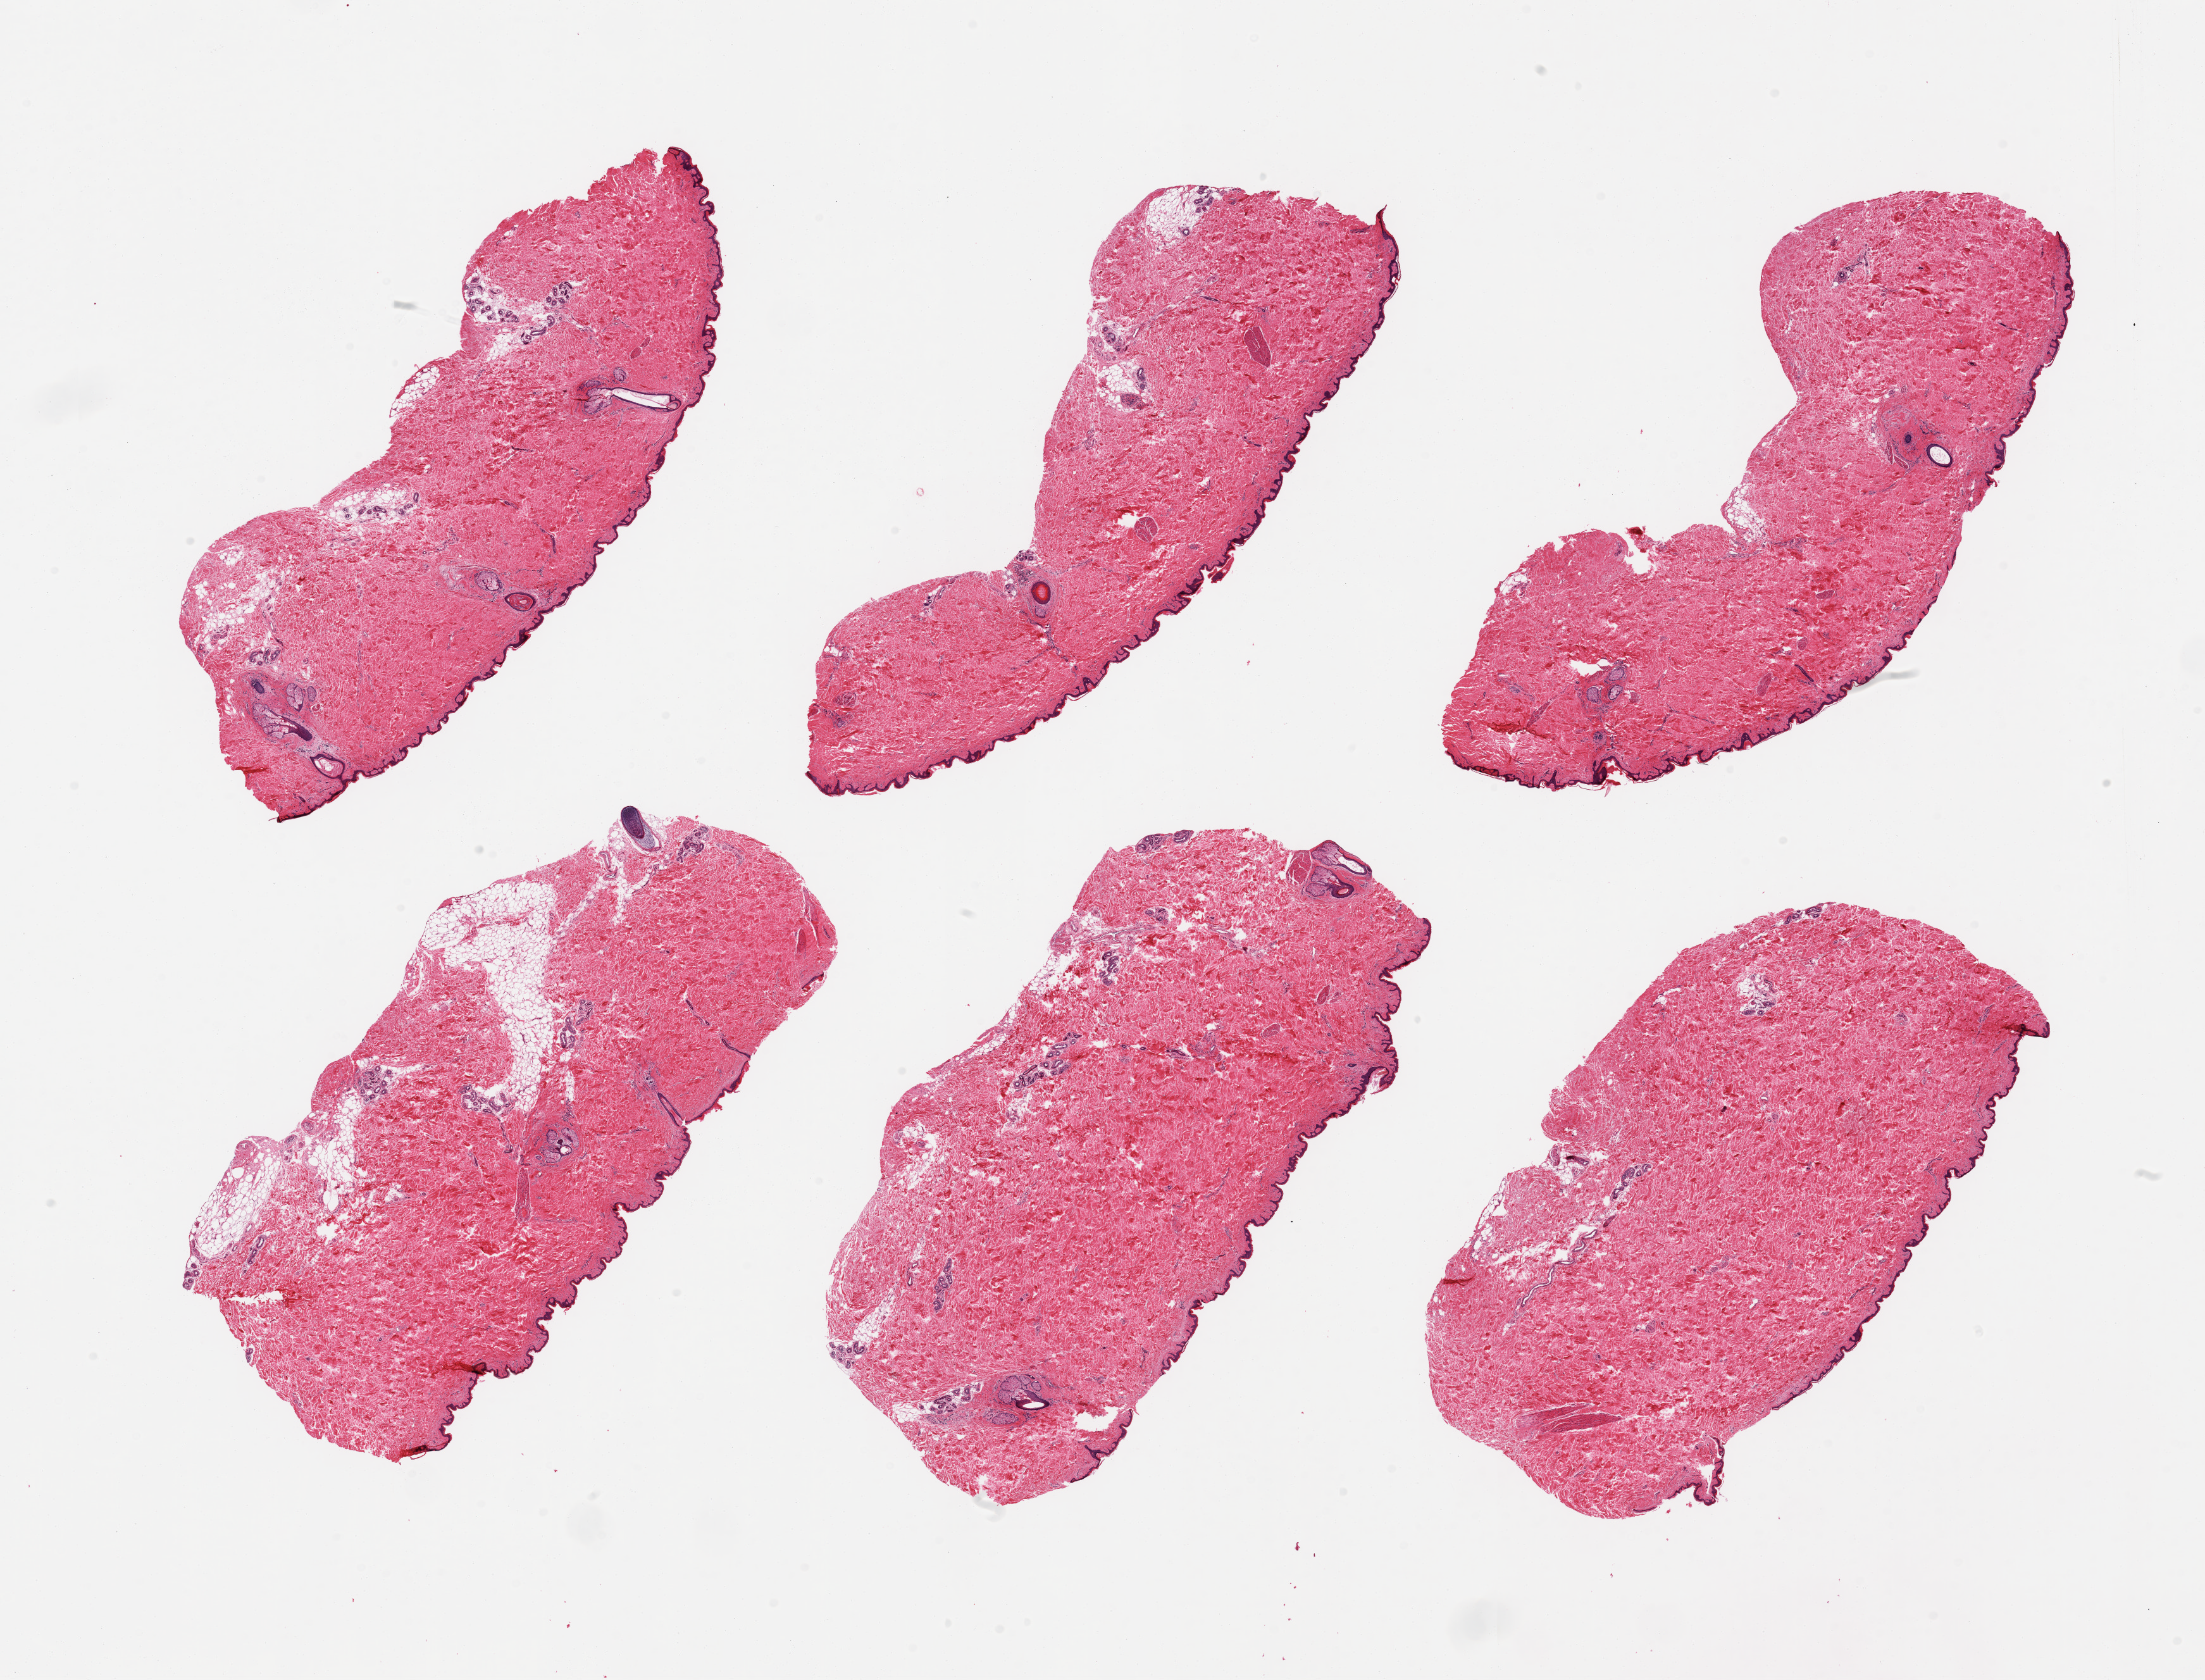
Whole-slide image, H&E stain, brightfield, low-resolution overview of the scanned area, about 27.6 x 21.0 mm; PAXgene-fixed, paraffin-embedded tissue; sampled site (target tissue): skin of suprapubic region; tissue donor sample. Donor sex: male.
• review note (as recorded): 6 pieces, trace dermal fat; squamous epithelium is ~40 microns